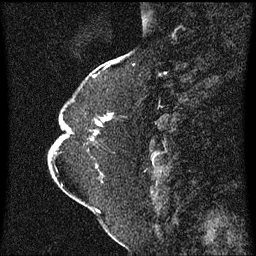
Breast MRI (dynamic contrast-enhanced), one sagittal slice; slice 22 of 60 in the series (ordered by position); dynamic contrast-enhanced series, image 2 of 3 at this slice position (ordered by acquisition); 1.5 T; TE 4.2 ms, TR 8.4 ms; 2 mm slice thickness; 256 × 256 image matrix. Female patient, age 52 years. Case-level facts recorded for this patient, not image findings: setting: breast cancer imaged before/during neoadjuvant chemotherapy; receptor status: HR-positive, HER2-negative.
Annotated regions visible in this slice (semi-automatically segmented with operator editing):
- analysis volume of interest (the breast-tissue region the enhancement analysis was run in; not a lesion): box from (x=64, y=104) to (x=114, y=167) px
- tumour enhancement mask (voxels above the 70 % enhancement threshold inside the analysis volume of interest): (x=97, y=114)–(x=113, y=125)